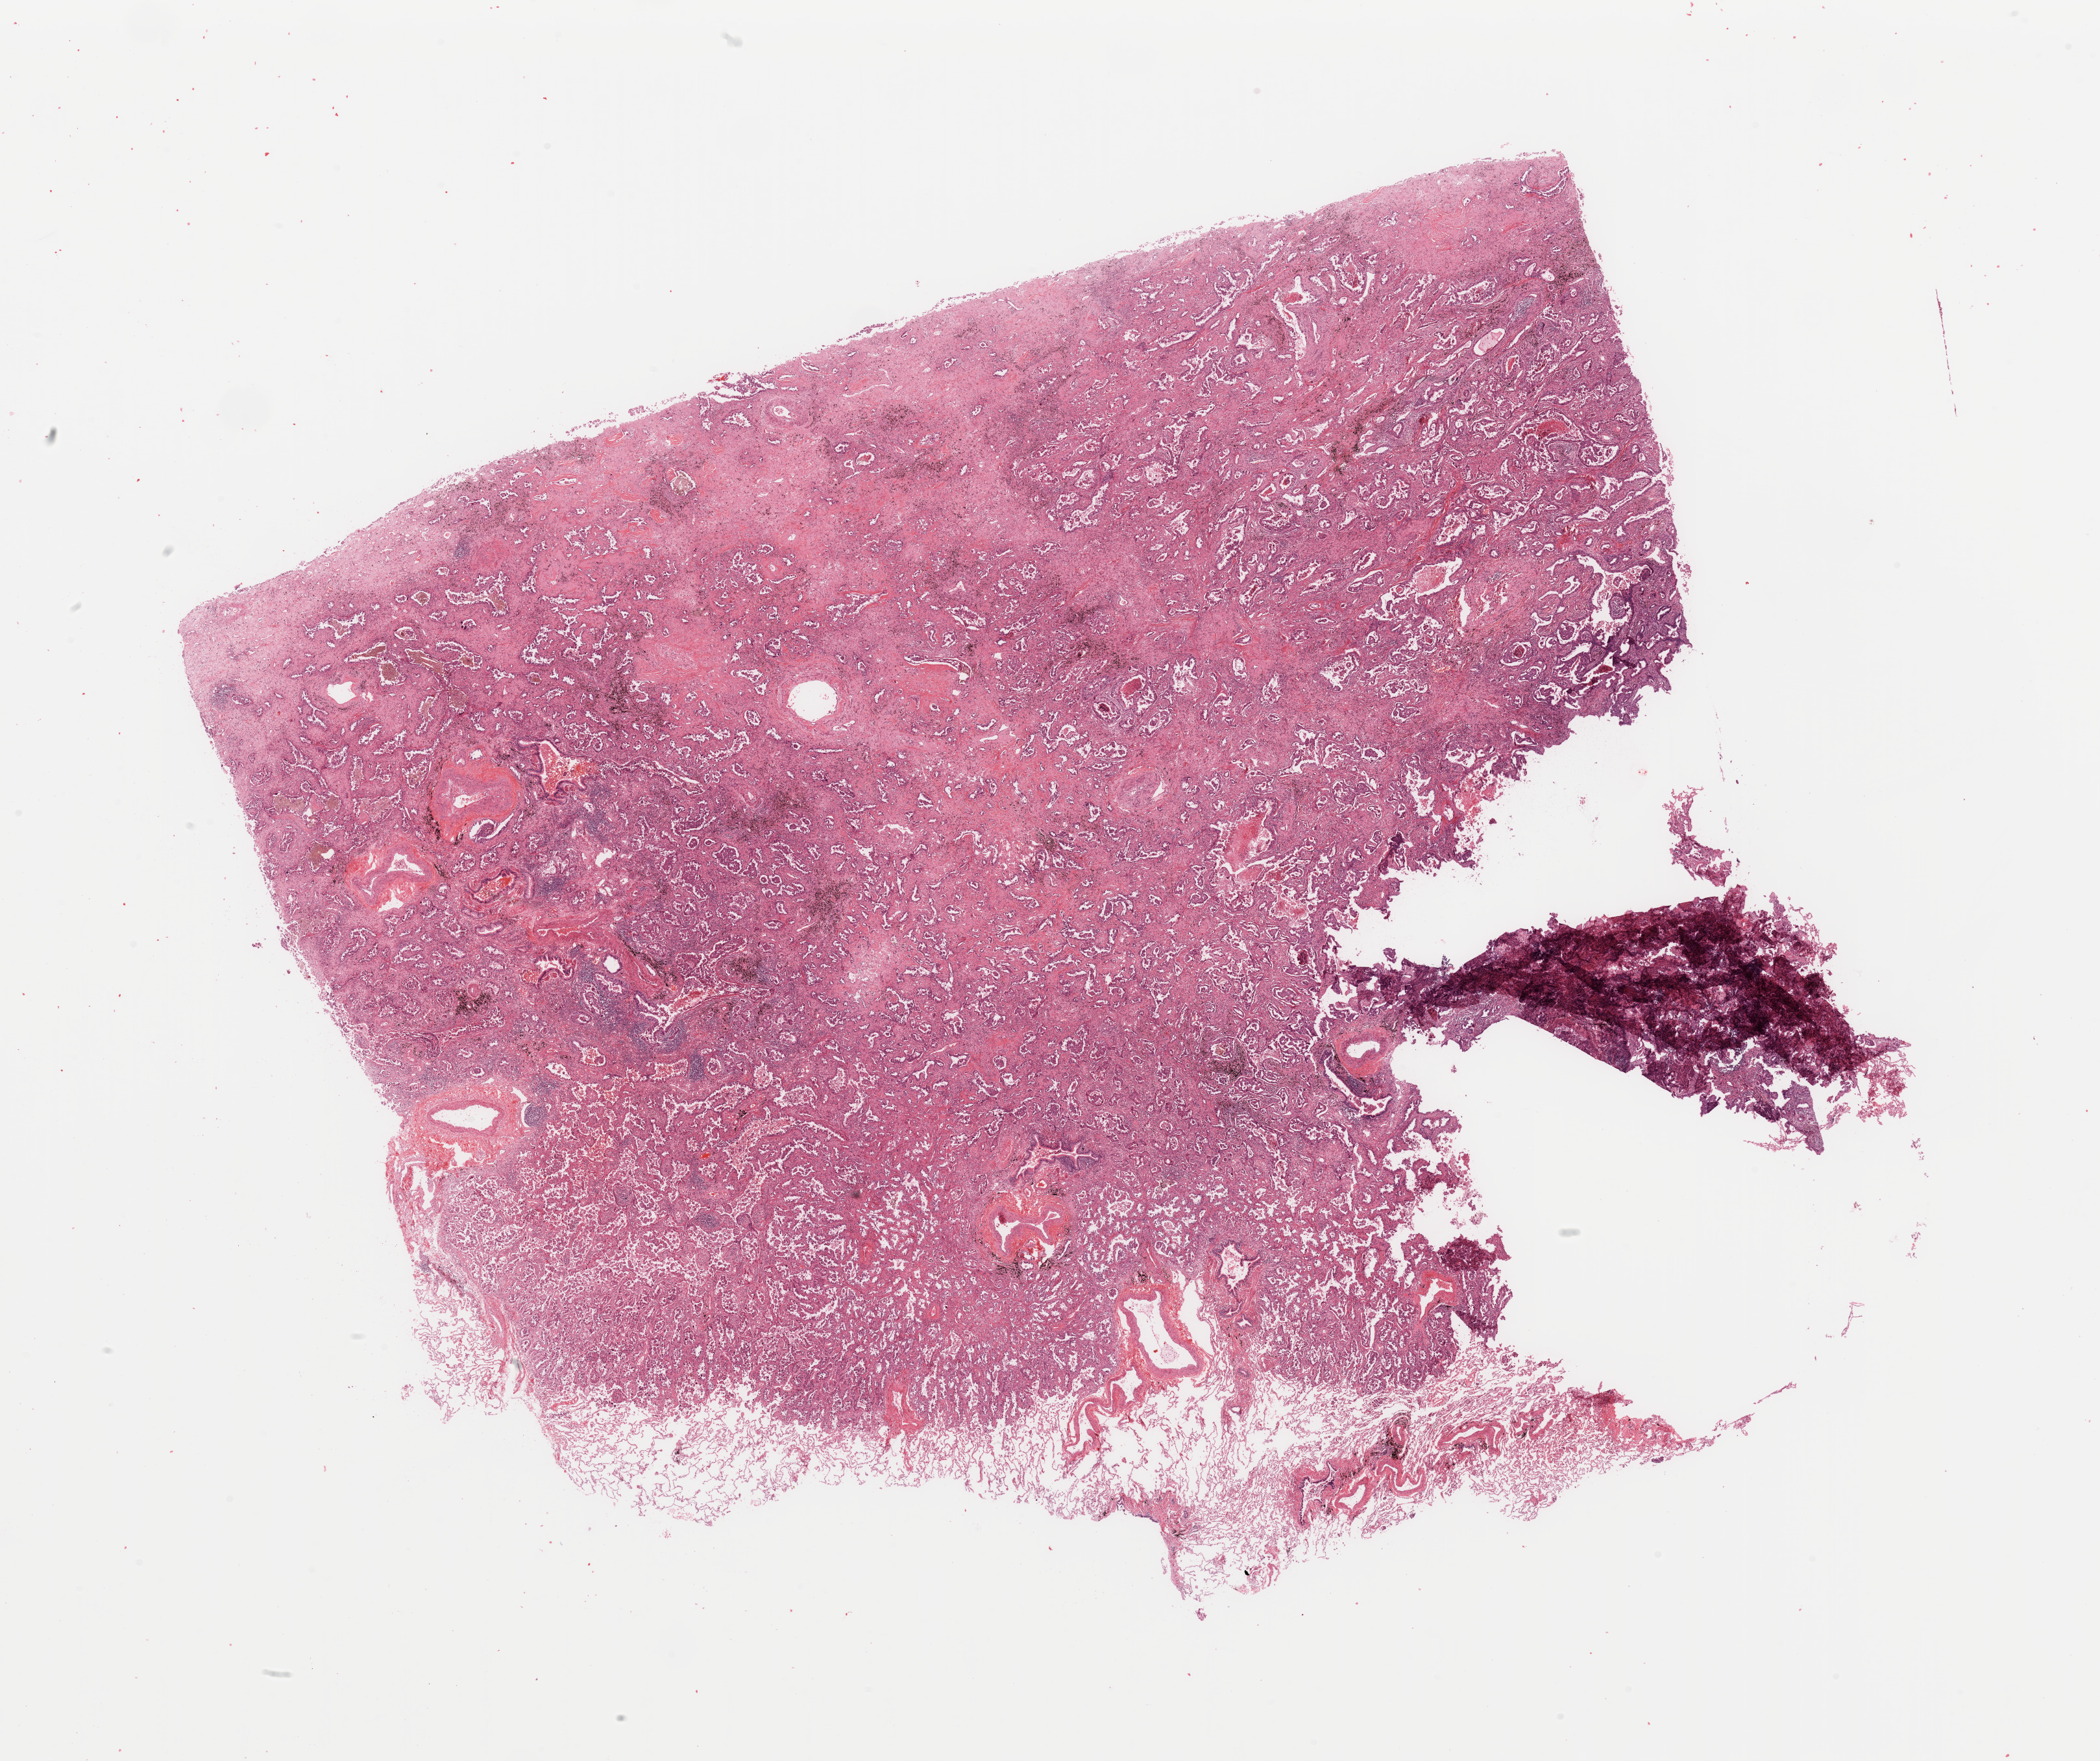
Hematoxylin and eosin (H&E) stained whole-slide image, shown as a low-resolution overview of the whole scanned area (about 25.6 x 21.5 mm, slide scanned at 20x), lung, tumour tissue. Patient: female, age 72 years. Histologic grade: G2 (moderately differentiated).
AJCC pathologic stage: IIIA. Diagnosis: Adenocarcinoma, NOS.